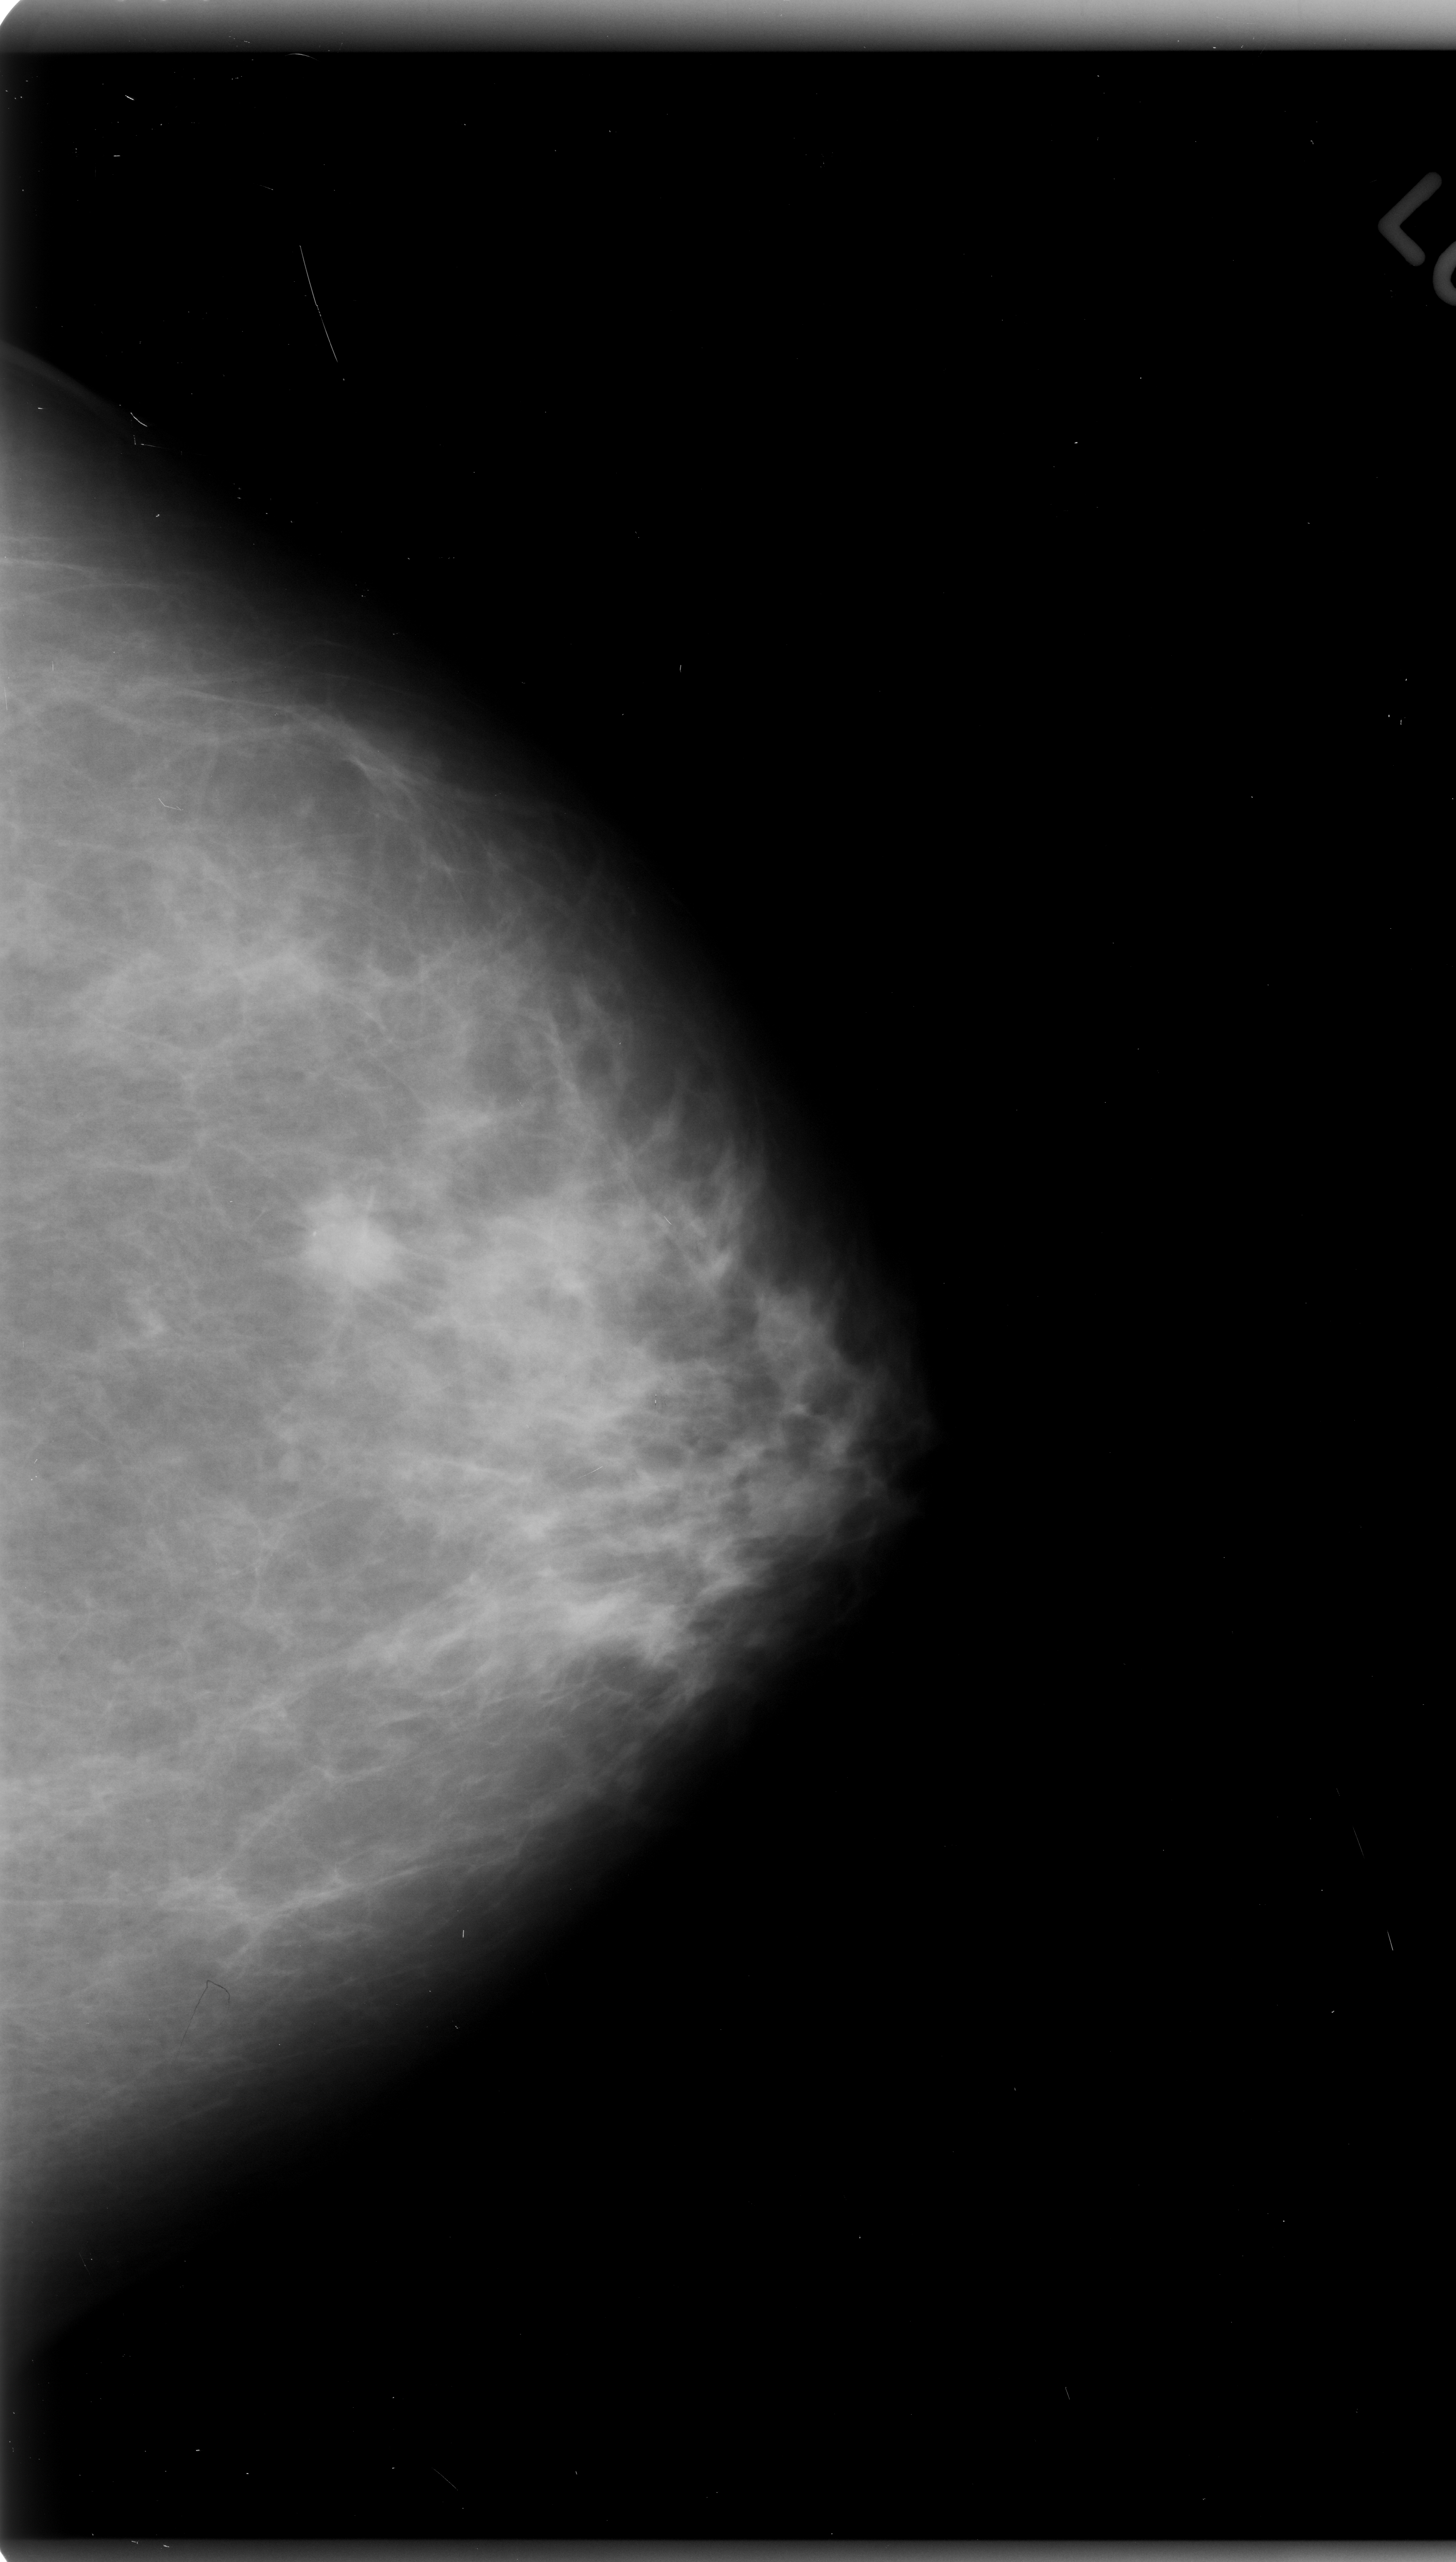
Digitized screen-film mammogram; left breast; craniocaudal (CC) view; breast composition: scattered fibroglandular densities (BI-RADS density category 2 of 4).
Finding: mass, shape oval, margins spiculated; BI-RADS assessment category 5; pathology (as recorded): malignant.